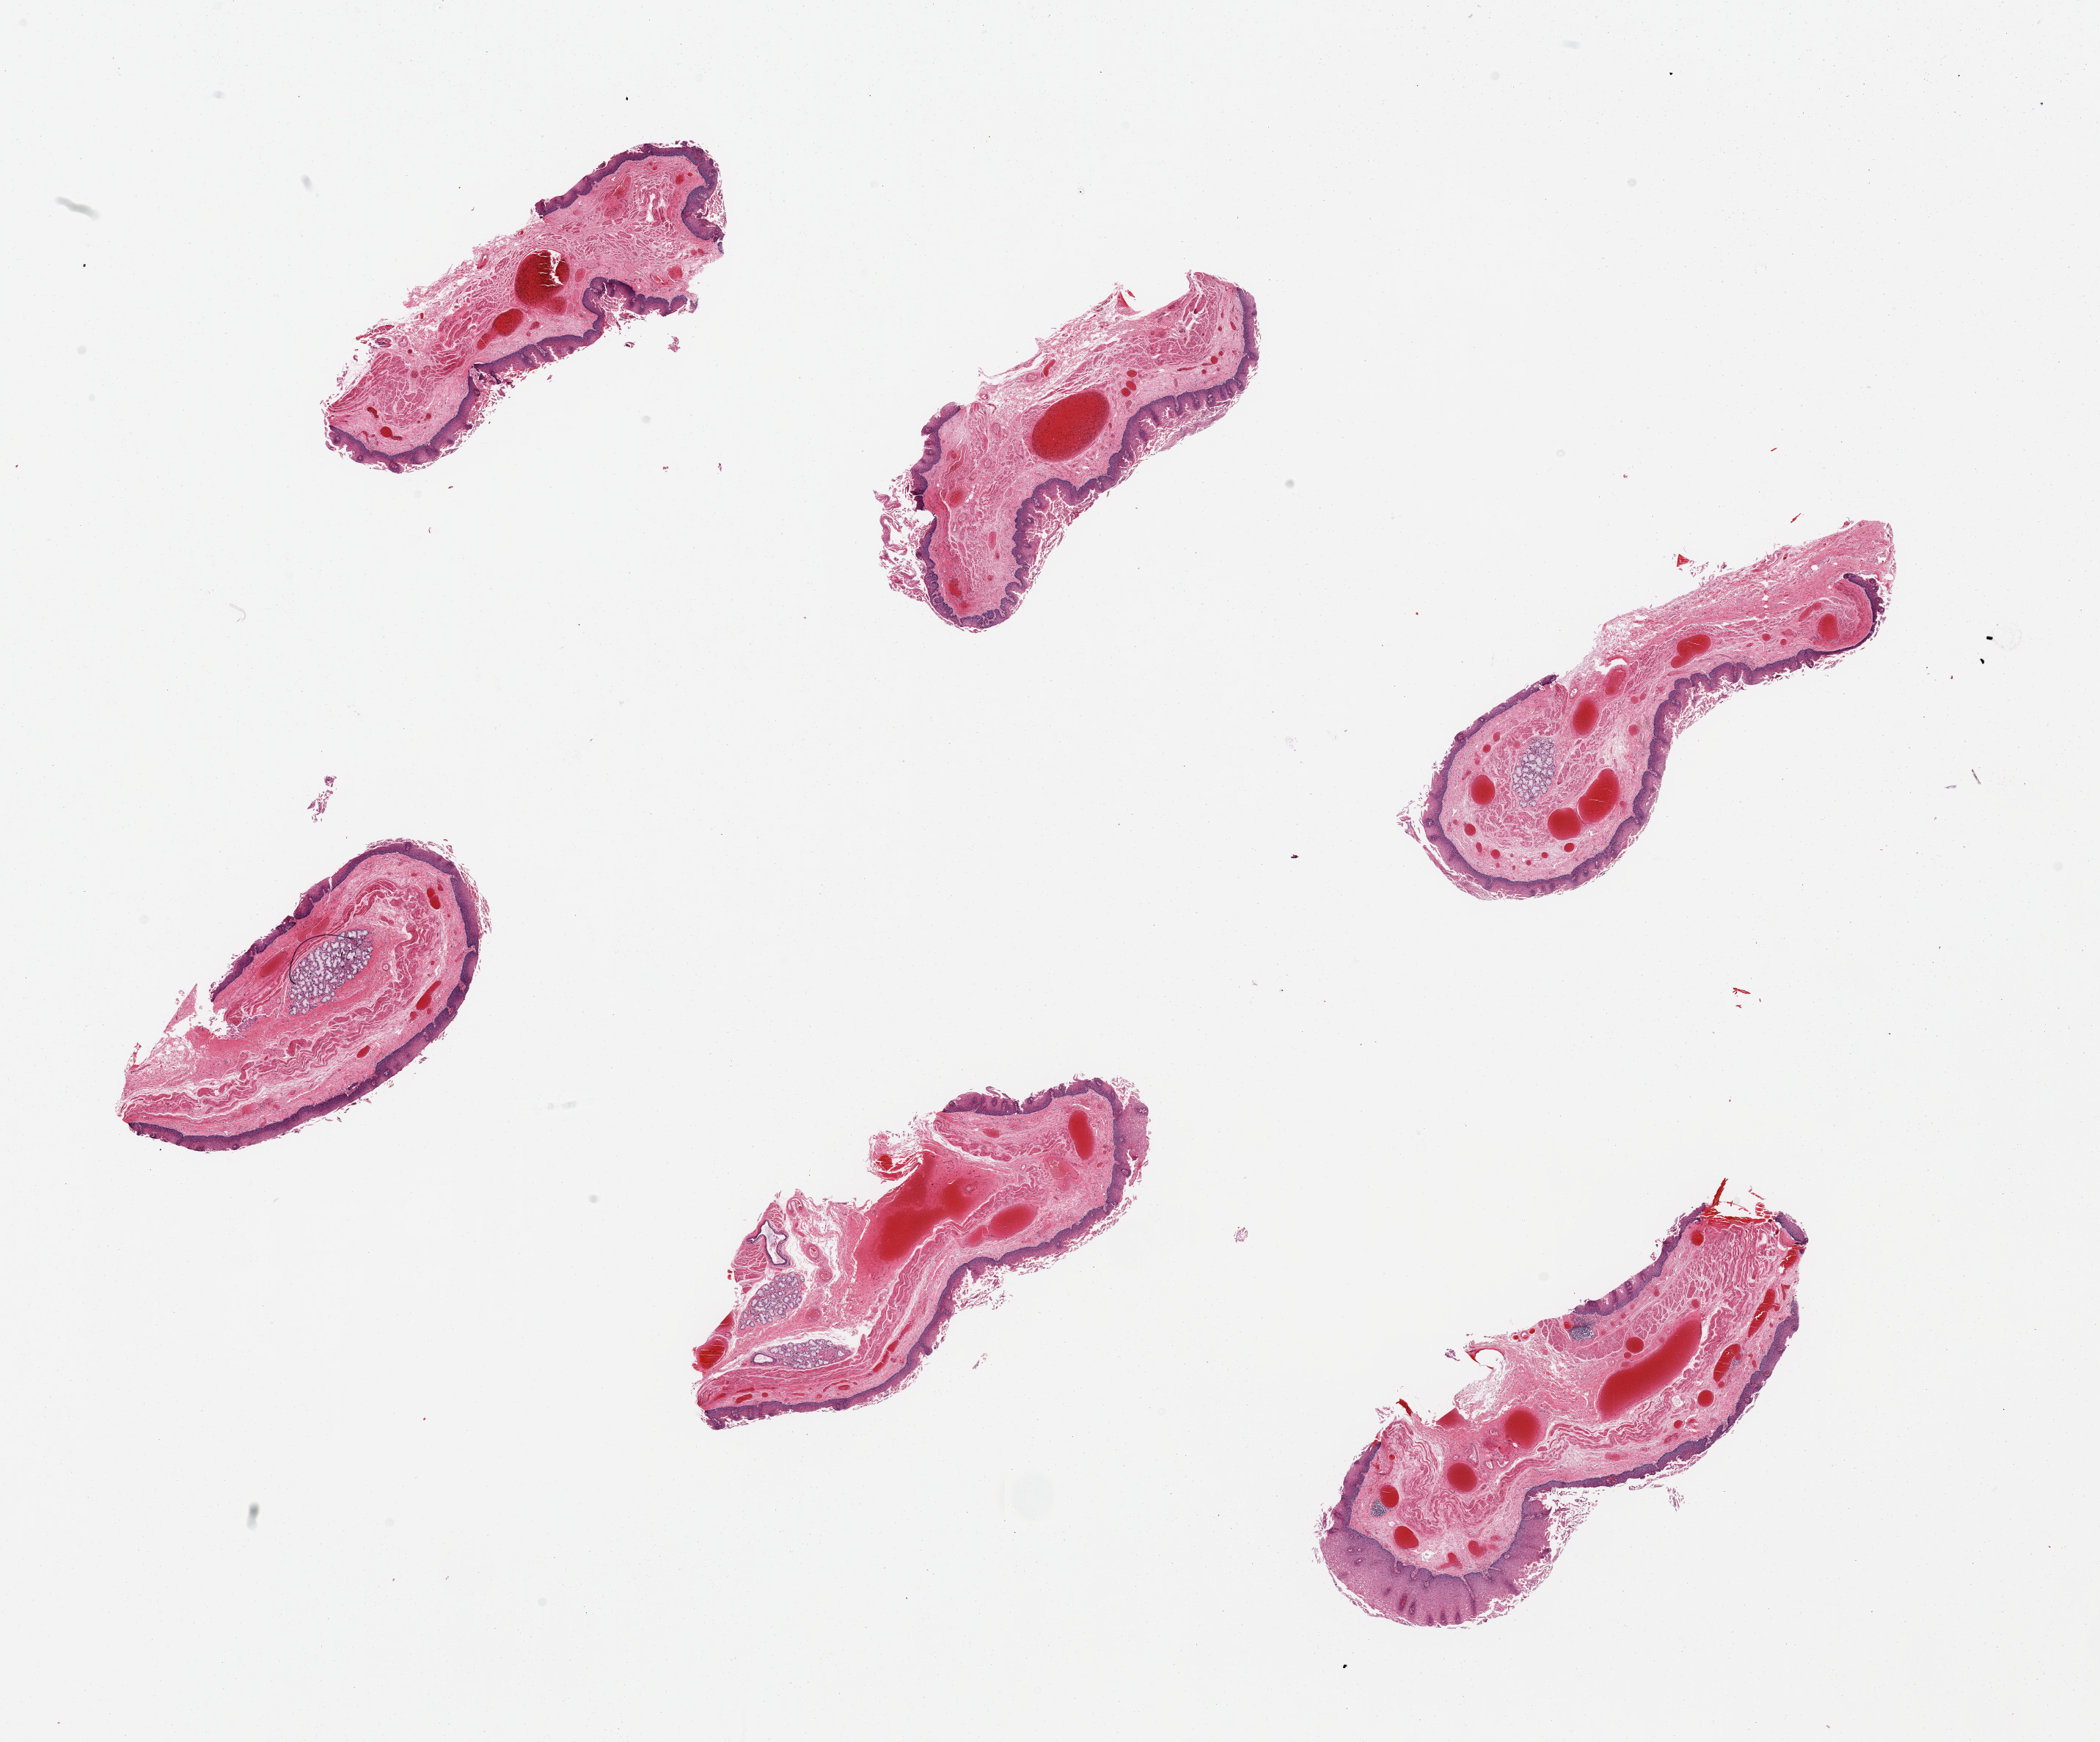
Digitized haematoxylin and eosin-stained section, a low-resolution overview of the entire scanned area, about 22.6 x 18.8 mm, PAXgene-fixed, paraffin-embedded tissue, section of esophageal mucous membrane (target tissue), tissue donor sample.
Pathologist's review note for this sample: 6 pieces, squamous mucosa is ~0.3mm, superficial sloughing; Submucosal mucus glands incidentally present.